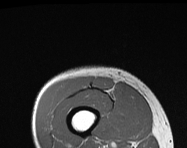
MRI of an extremity soft-tissue mass, one axial slice. Slice 29 of 114 in the series (ordered by position). MR volume resampled by the dataset authors to the PET/CT grid (not the native acquisition matrix). 3.27 mm slice thickness. 187 × 148 image matrix. Male patient. Case-level facts recorded for this patient, not image findings: histological type: pleiomorphic leiomyosarcoma; grade: intermediate; site of the primary tumour: right thigh.
Structures marked on this image (expert contour drawn on MRI and transferred to this co-registered scan by the dataset authors):
- gross tumour volume including surrounding oedema: box from (x=93, y=77) to (x=112, y=91) px